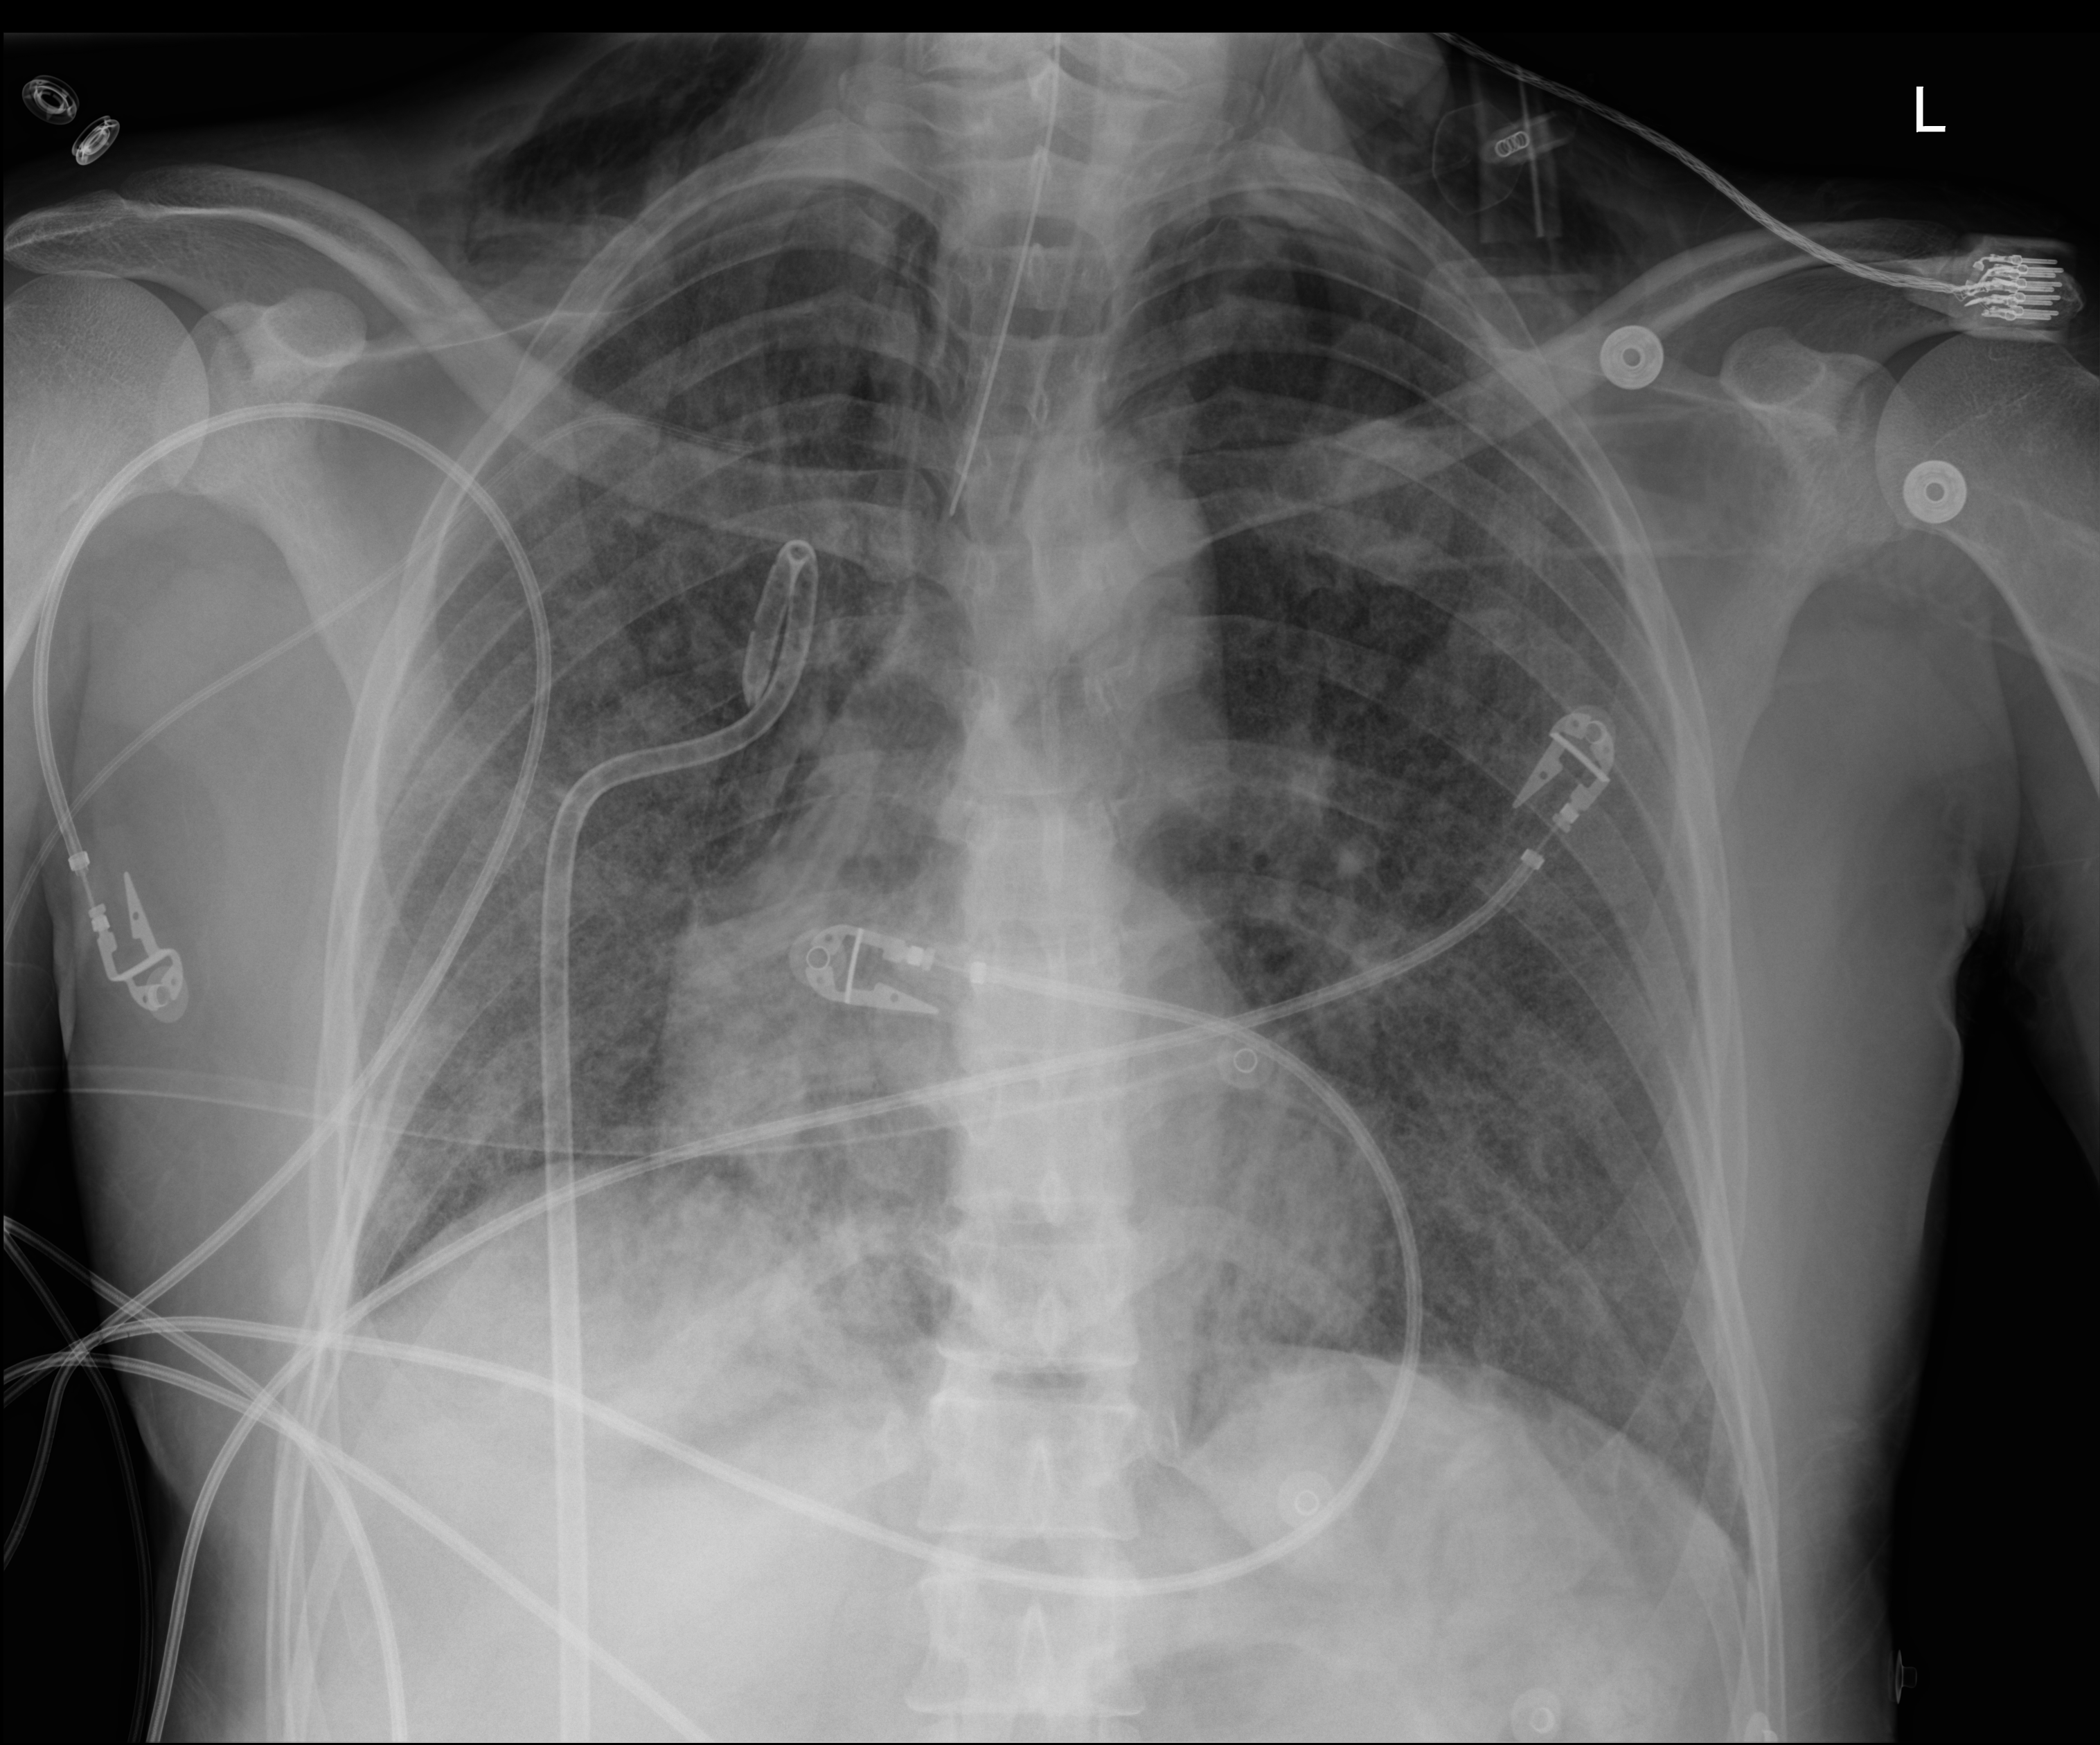
Chest X-ray (portable), anteroposterior (AP) projection. Adult patient hospitalised with COVID-19, age 18–59 years.
Admission-level facts for this patient (not findings on this image; timing relative to this image not recorded):
- admitted to intensive care during this hospital stay: yes